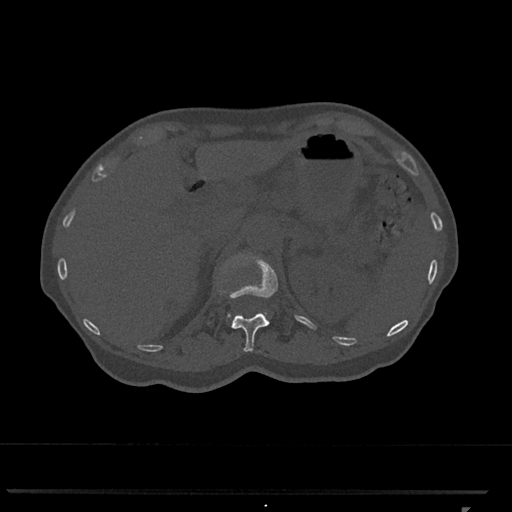
CT including the spine, one axial slice; slice 445 of 793 in the series (ordered by position); bone window (W 1800 / L 400 HU); 512 × 512 image matrix. Female patient, age 62 years. Case-level facts recorded for this patient, not image findings: primary cancer: renal.
Structures marked on this image (semi-automatic segmentation, software-assisted and operator-edited):
- L1 vertebra: bounding box (x1, y1, x2, y2) in pixels: (227, 255, 267, 319)
- T12 vertebra: (219, 255, 278, 352)